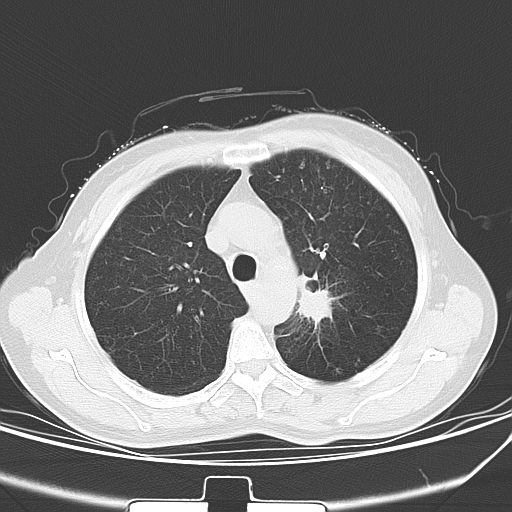
Chest CT, one axial slice; position 42 of 53 along the scan axis; lung window (W 1500 / L -600 HU); 512 × 512 image matrix, field of view 329 × 329 mm. Female patient, age 60 years. From the clinical record (not read from this slice): clinical TNM (as recorded): T1b N0 M0.
Outlined on this slice (bounding box drawn by a radiologist):
- lung tumour (recorded histology: squamous cell carcinoma): bounding box (x1, y1, x2, y2) in pixels: (294, 263, 335, 330)